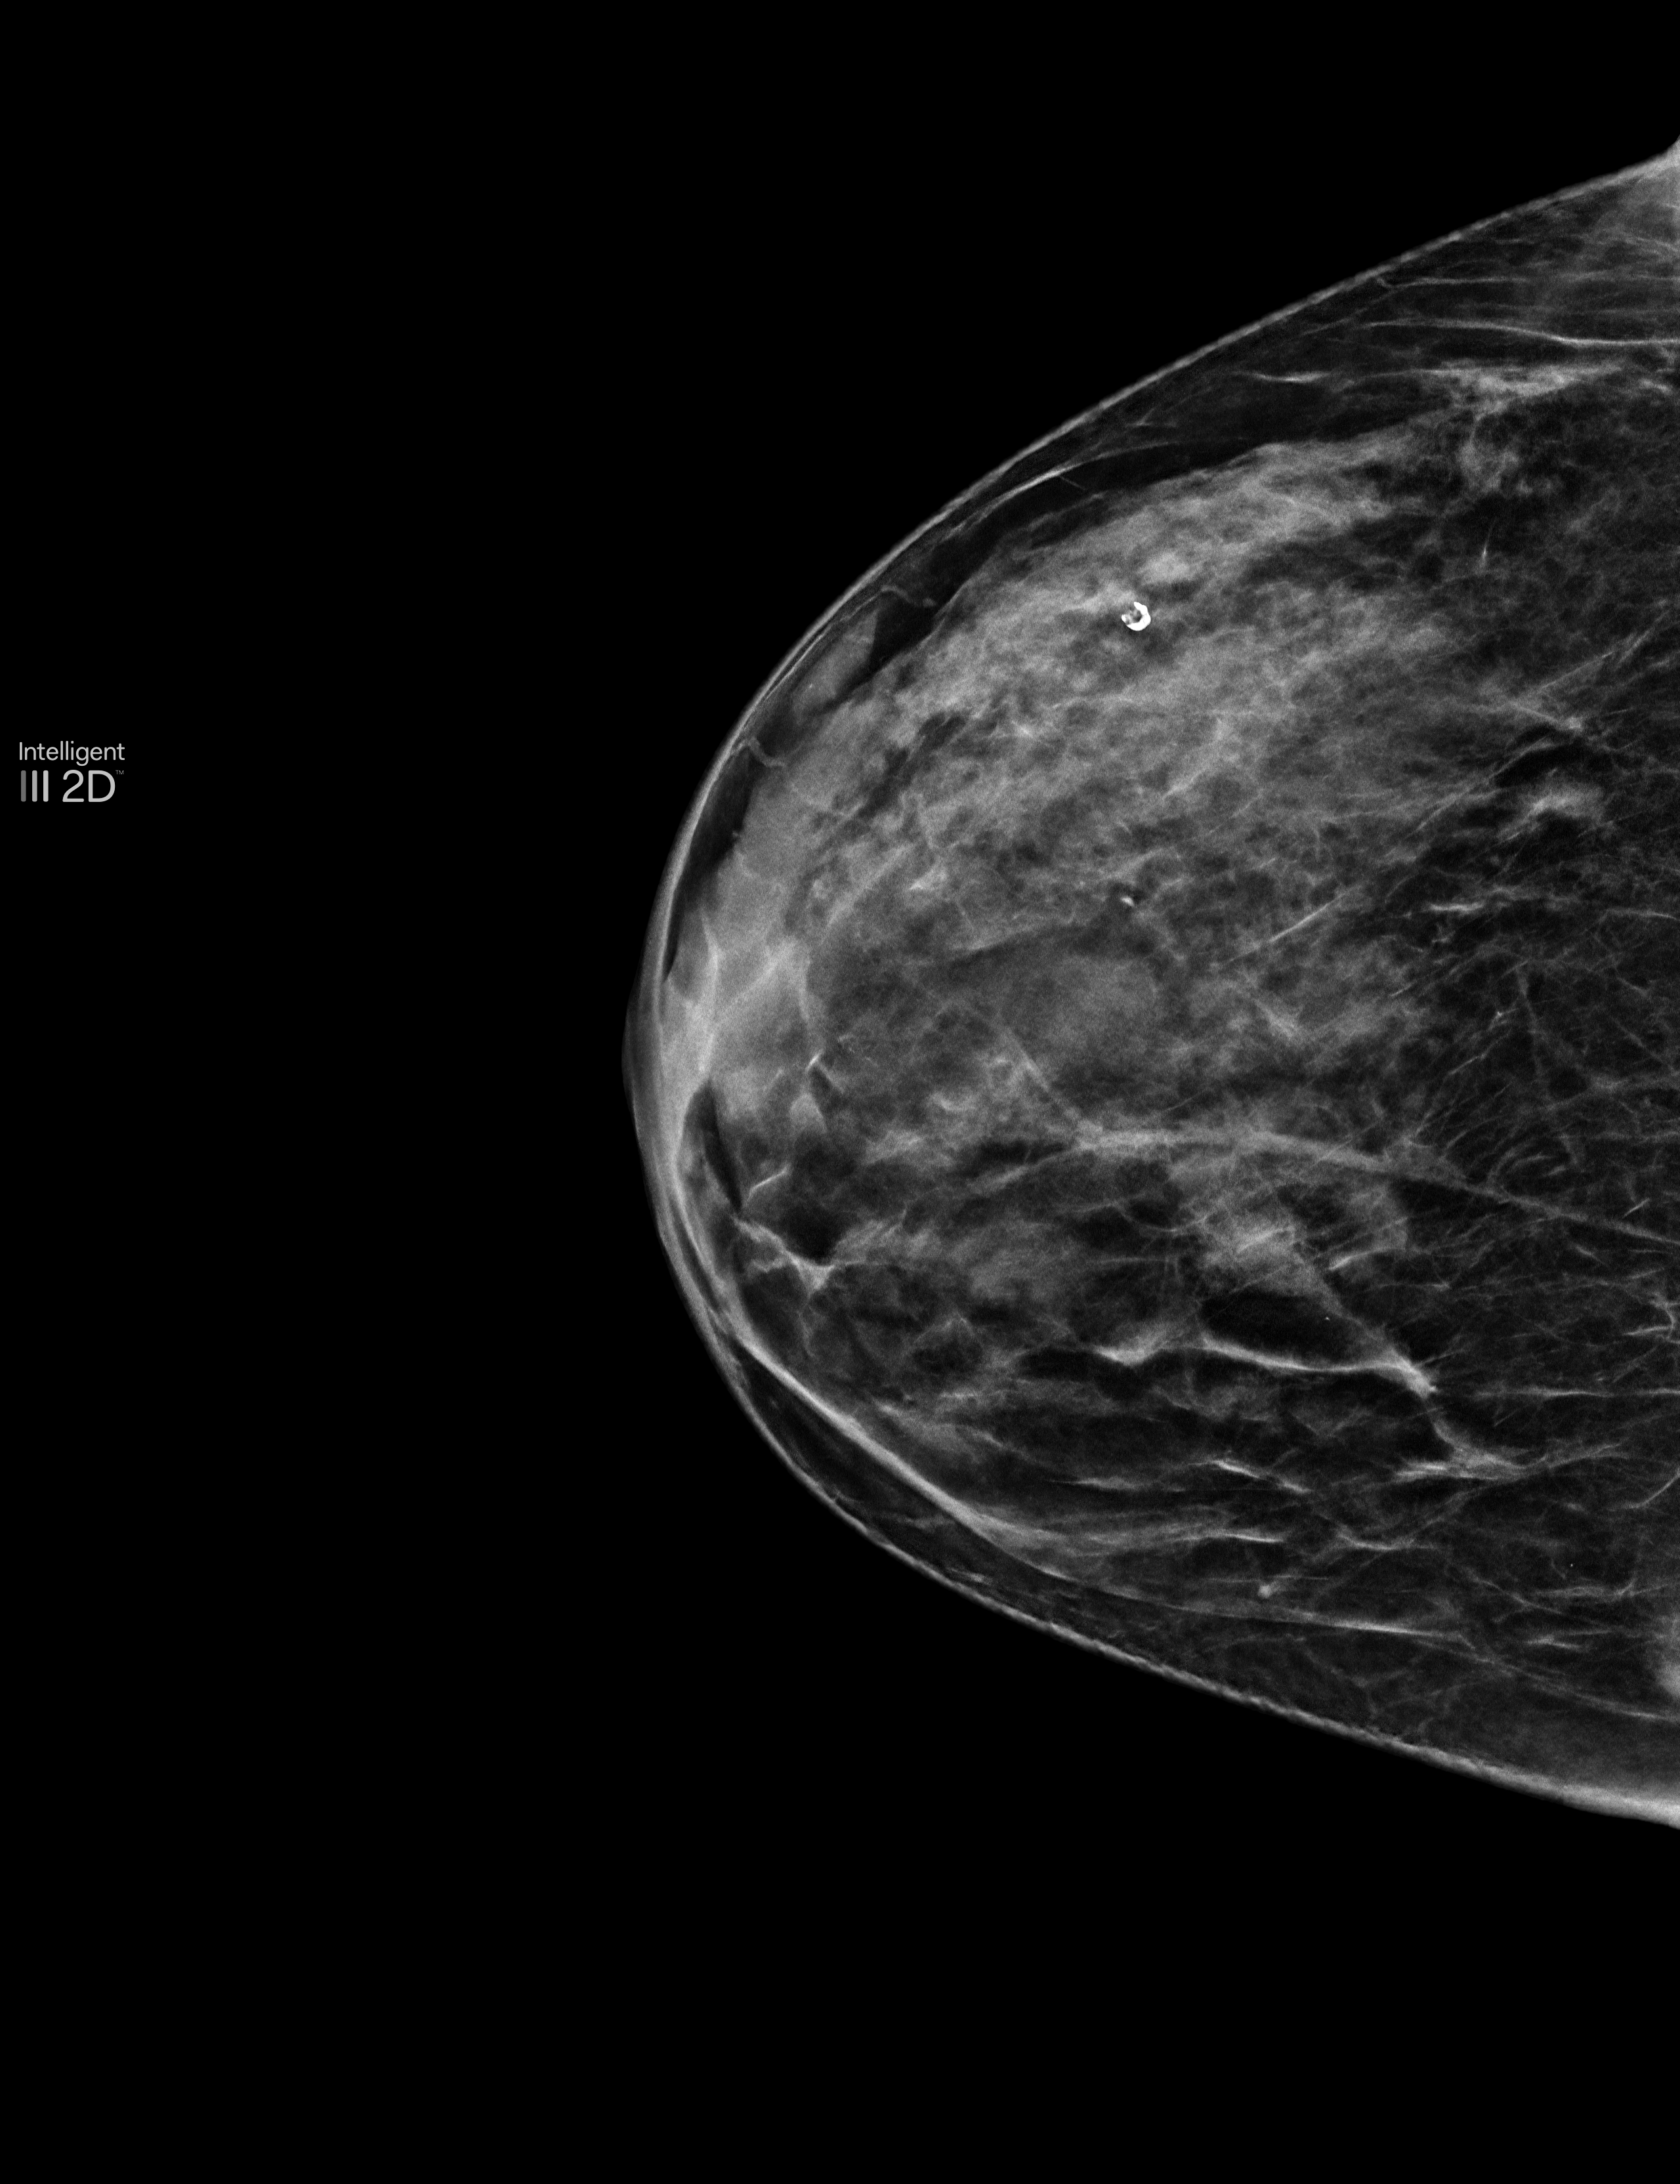
Screening examination, compressed breast thickness 44 mm, system: Selenia Dimensions. Patient aged 51 years (female).
Image type: synthesized 2-D view from tomosynthesis. Breast: right. Projection: cranio-caudal projection.